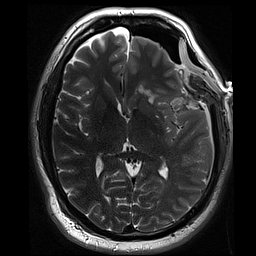
Brain MRI from a brain-tumour surgery series, one axial slice; position 43 of 70 along the scan axis; 2 mm slice thickness; 256 × 256 image matrix. From the clinical record (not read from this slice): histopathology: Oligodendroglioma; WHO grade: 3; IDH mutation: yes; tumour location: Left Sylvian Fissure (Temporal).
Annotated regions visible in this slice (outlined manually by an expert reader):
- residual tumour: bounding box <142,90,177,106> (left, top, right, bottom; pixels)